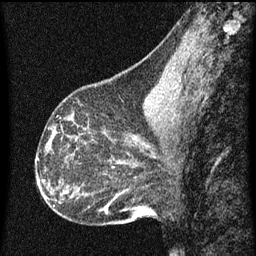
Breast MRI (dynamic contrast-enhanced), one sagittal slice. Dynamic contrast-enhanced series, image 2 of 3 at this slice position (ordered by acquisition). 1.5 T. TE 4.2 ms, TR 8 ms. 2 mm slice thickness. 256 × 256 image matrix. Female patient, age 43 years.
Structures marked on this image (semi-automatic segmentation, software-assisted and operator-edited):
- analysis volume of interest (the breast-tissue region the enhancement analysis was run in; not a lesion): box from (x=53, y=104) to (x=101, y=151) px
- tumour enhancement mask (voxels above the 70 % enhancement threshold inside the analysis volume of interest): (x=68, y=120)–(x=73, y=137)